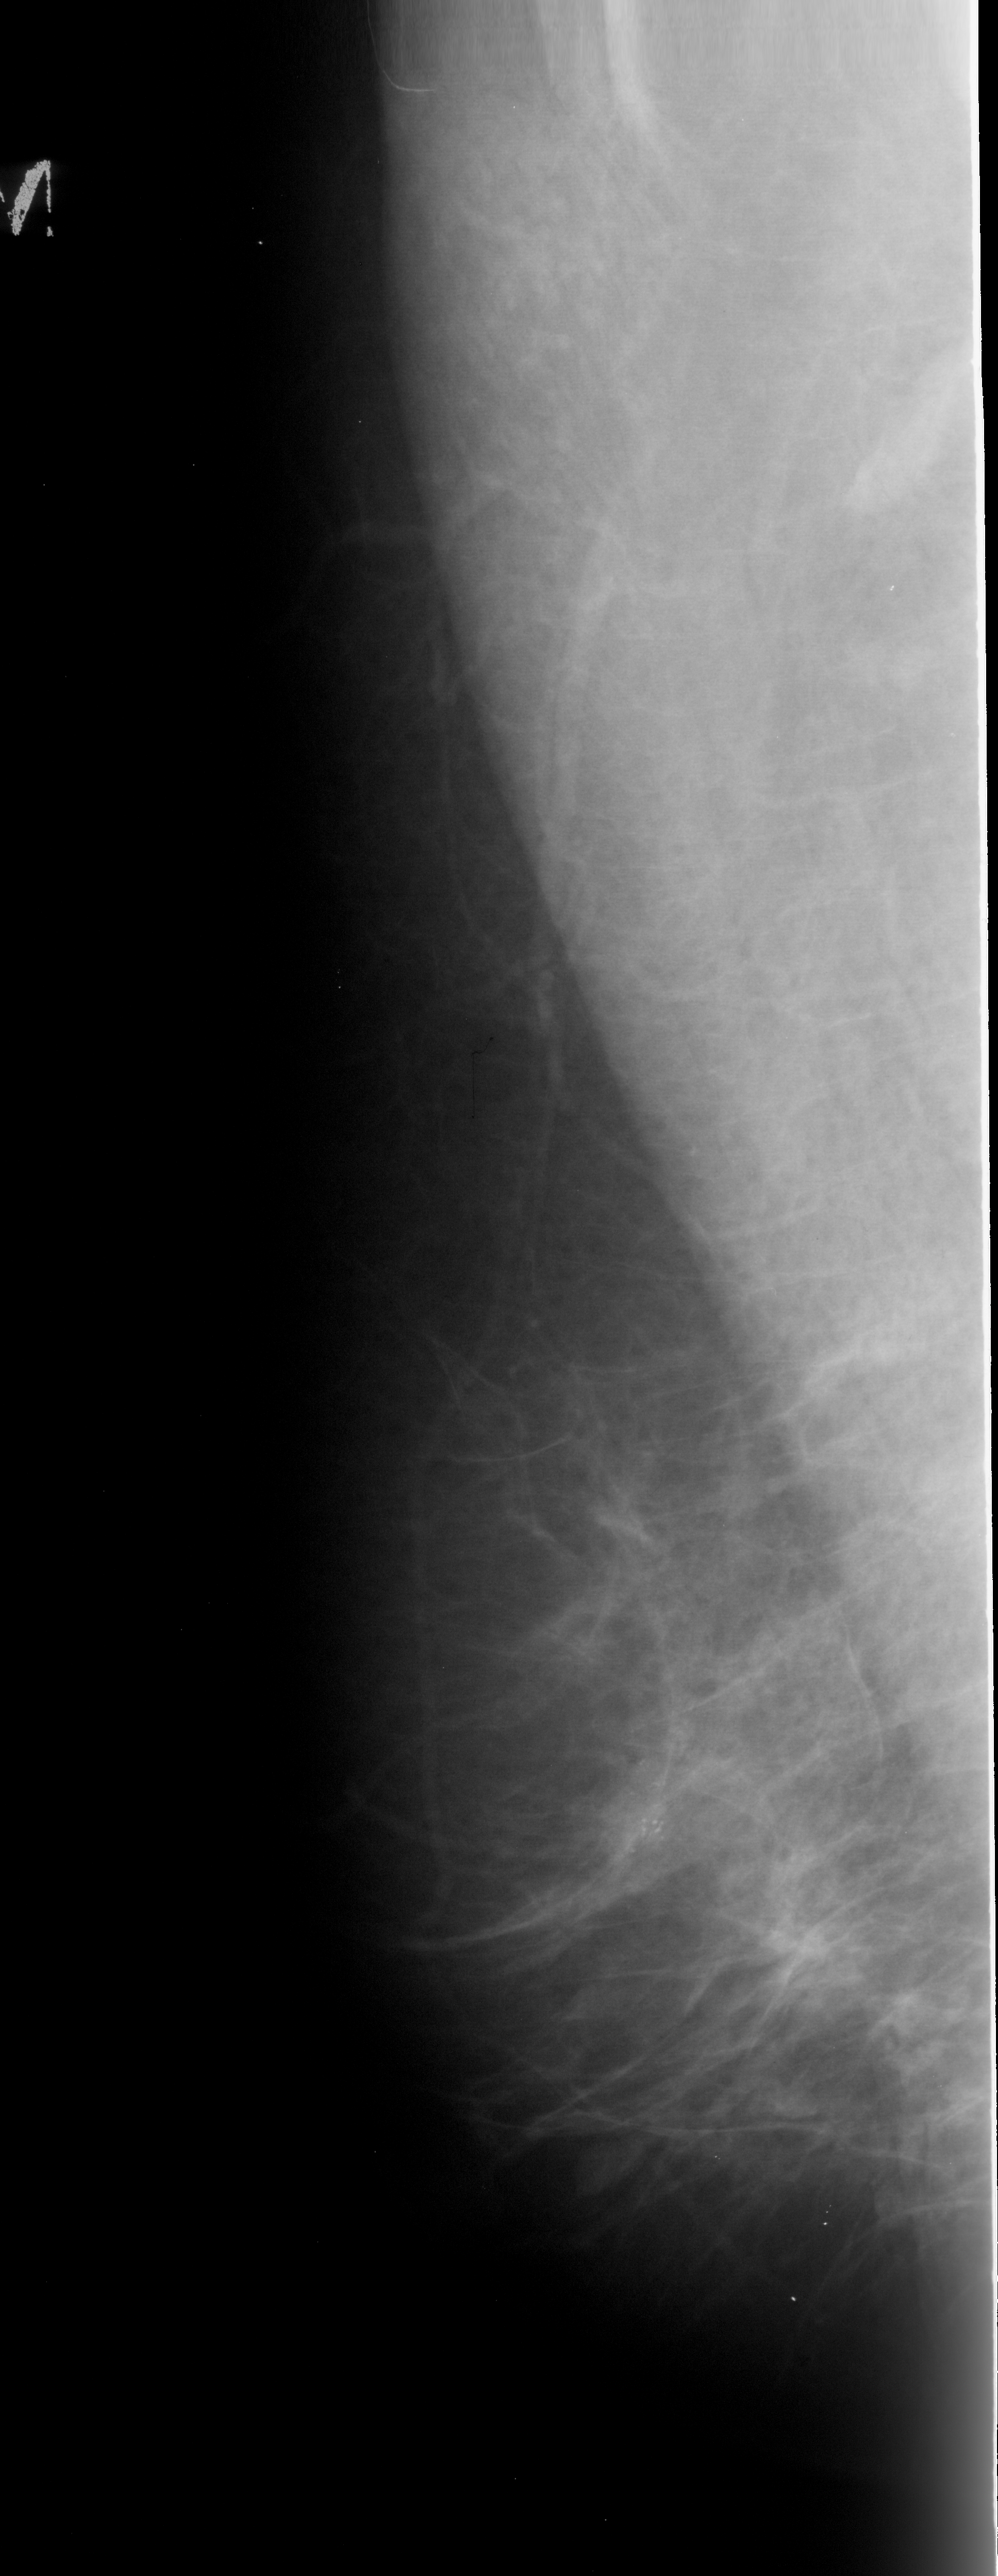
Digitized screen-film mammogram. Left breast. Mediolateral oblique (MLO) view. Breast composition: scattered fibroglandular densities (BI-RADS density category 2 of 4). 998 × 2576 image matrix.
Expert-marked regions of interest on this image (one box per marked abnormality):
- calcifications, morphology pleomorphic, distribution clustered; BI-RADS assessment category 4; subtlety rating 3 on a 1 (subtle) to 5 (obvious) scale; pathology (as recorded): malignant: bounding box <601,1759,680,1876> (left, top, right, bottom; pixels)